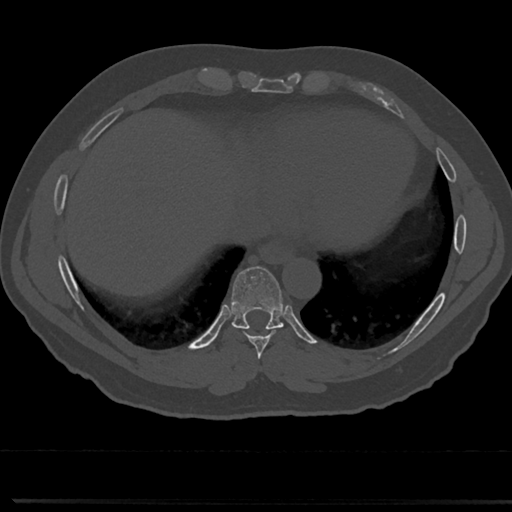
CT including the spine, one axial slice; slice 327 of 817 in the series (ordered by position); bone window (W 1800 / L 400 HU); 0.5 mm slice thickness; 512 × 512 image matrix, field of view 355 × 355 mm. Male patient, age 61 years. From the clinical record (not read from this slice): primary cancer: prostate.
Structures marked on this image (semi-automatically segmented with operator editing):
- T7 vertebra: bounding box <258,351,266,376> (left, top, right, bottom; pixels)
- T8 vertebra: <211,270,310,357>